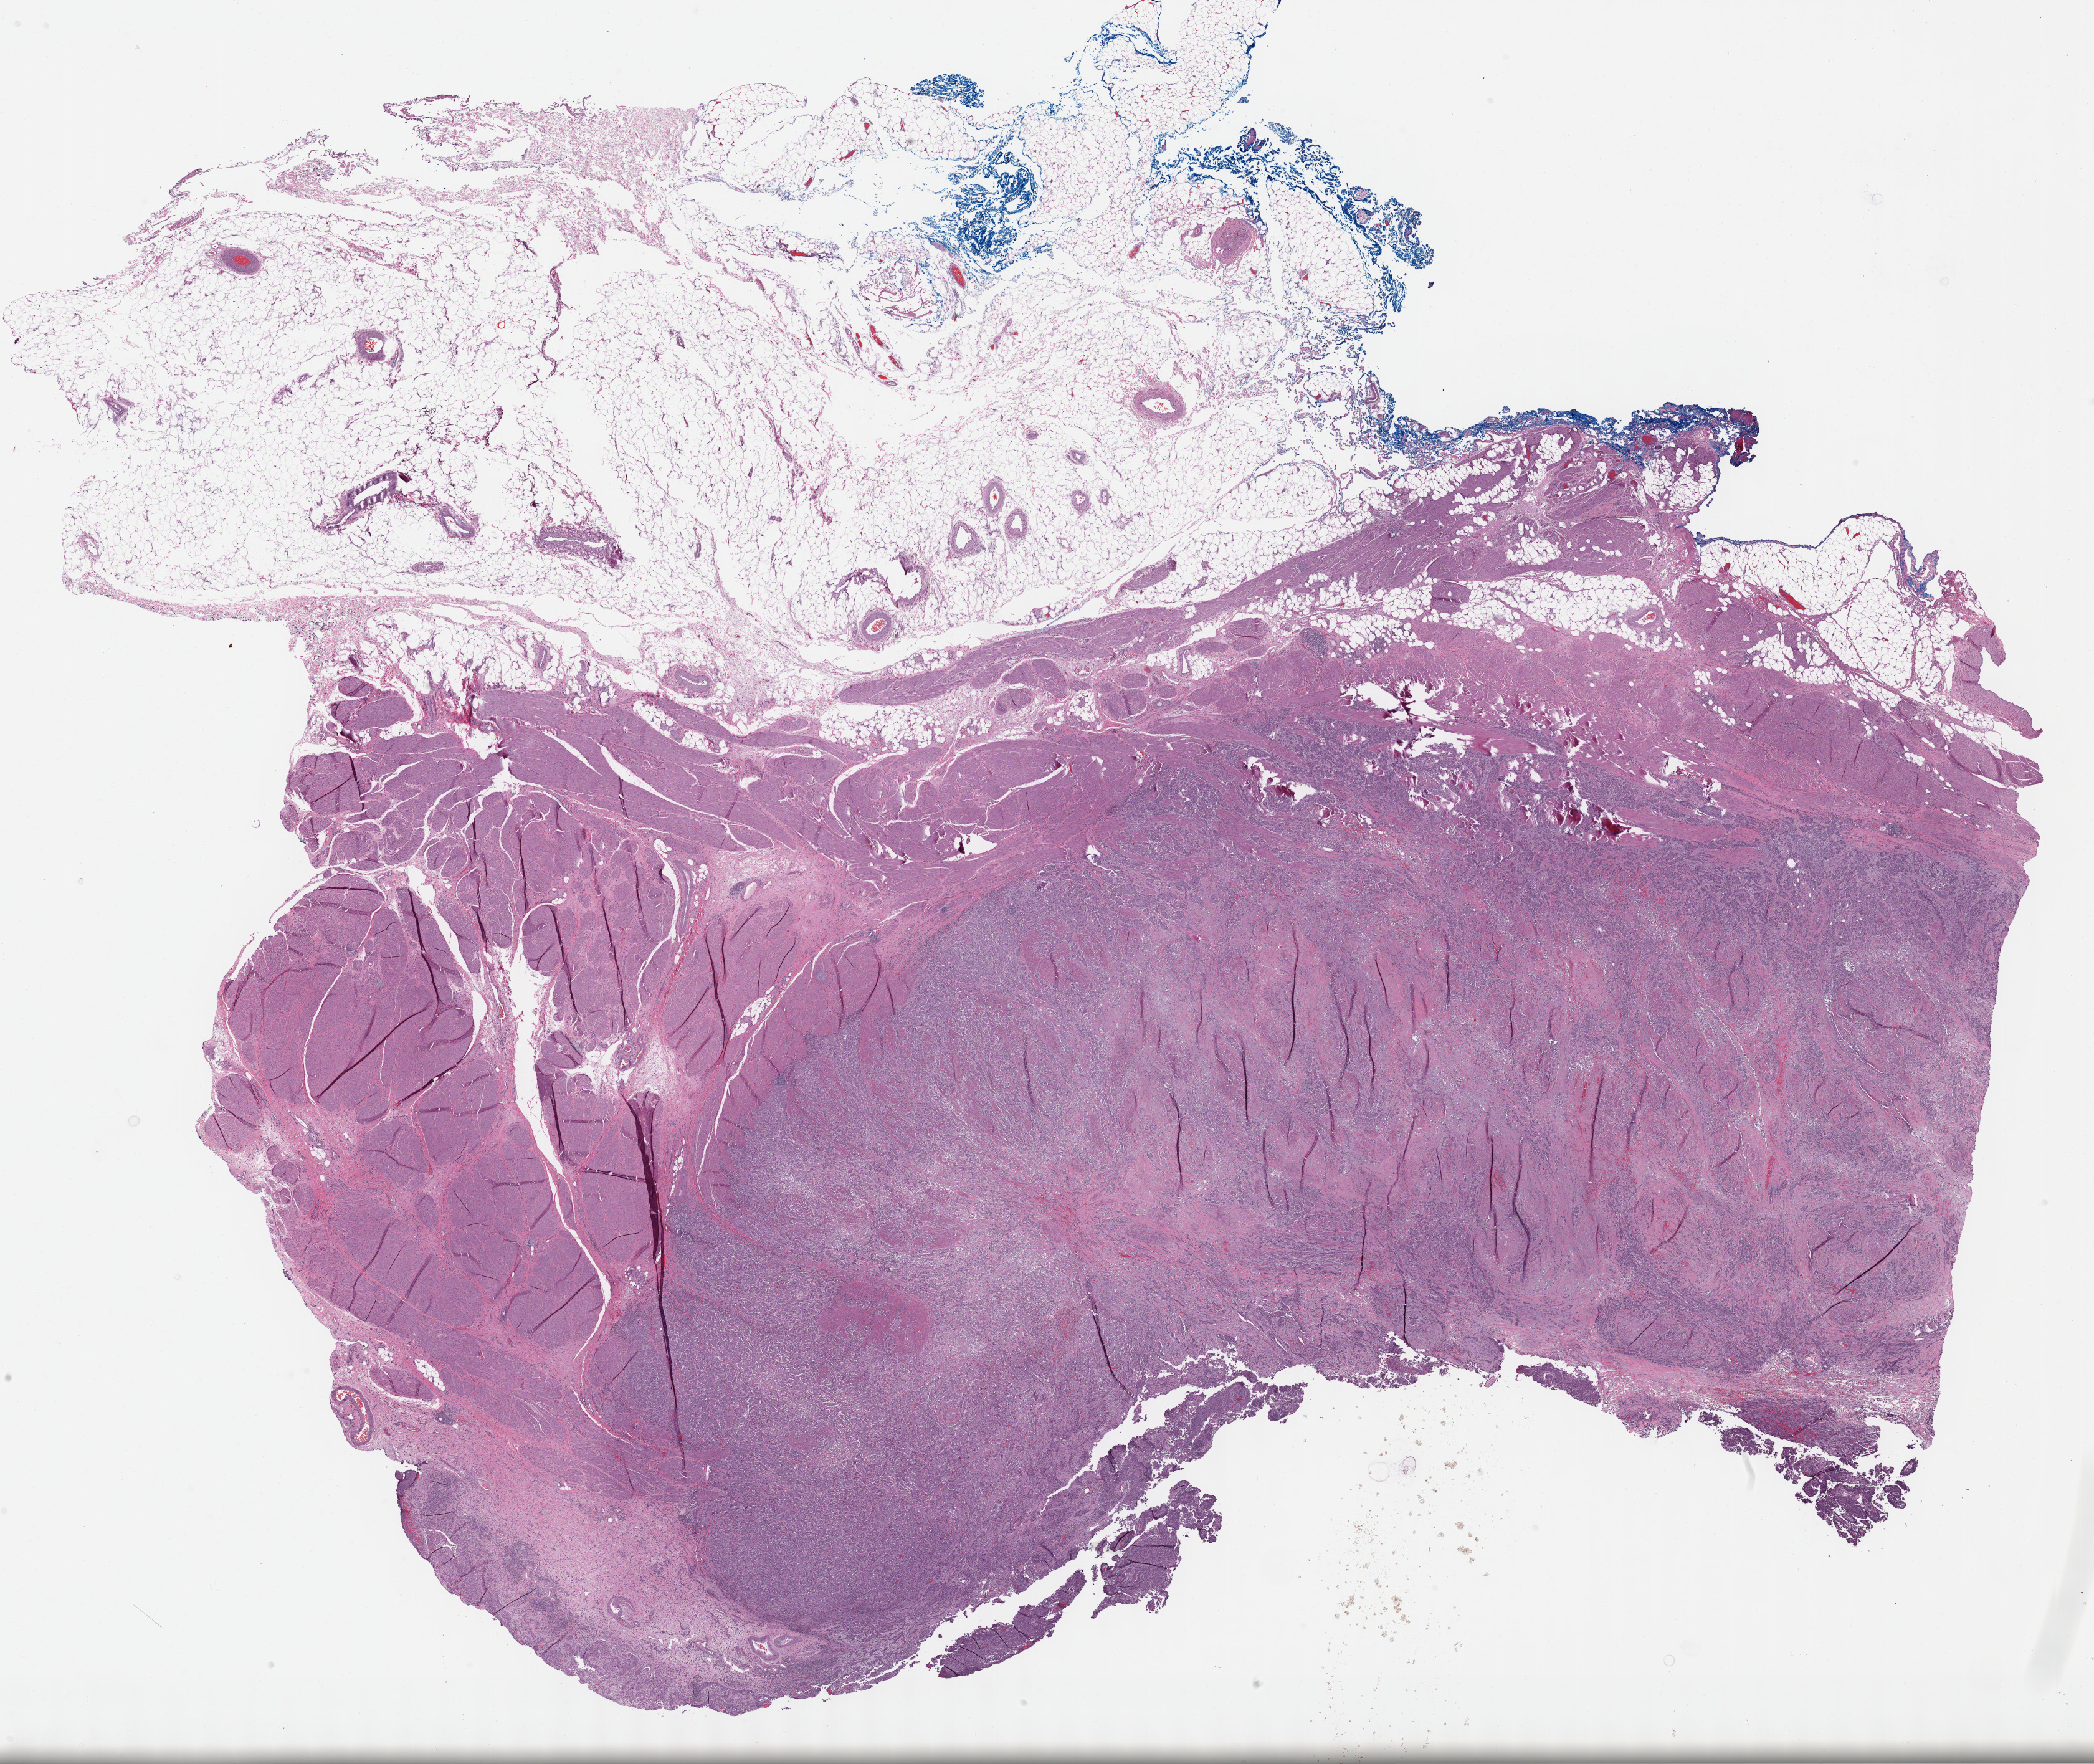
Digitized Hematoxylin and eosin (H&E) stained tissue section (whole slide) — low-resolution overview of the scanned area, about 27.2 x 22.9 mm (from a 40x scan), formalin-fixed paraffin-embedded (FFPE) diagnostic section, primary tumour sample from the bladder. Male patient; age at initial diagnosis 45 years.
Diagnosis: Transitional cell carcinoma.